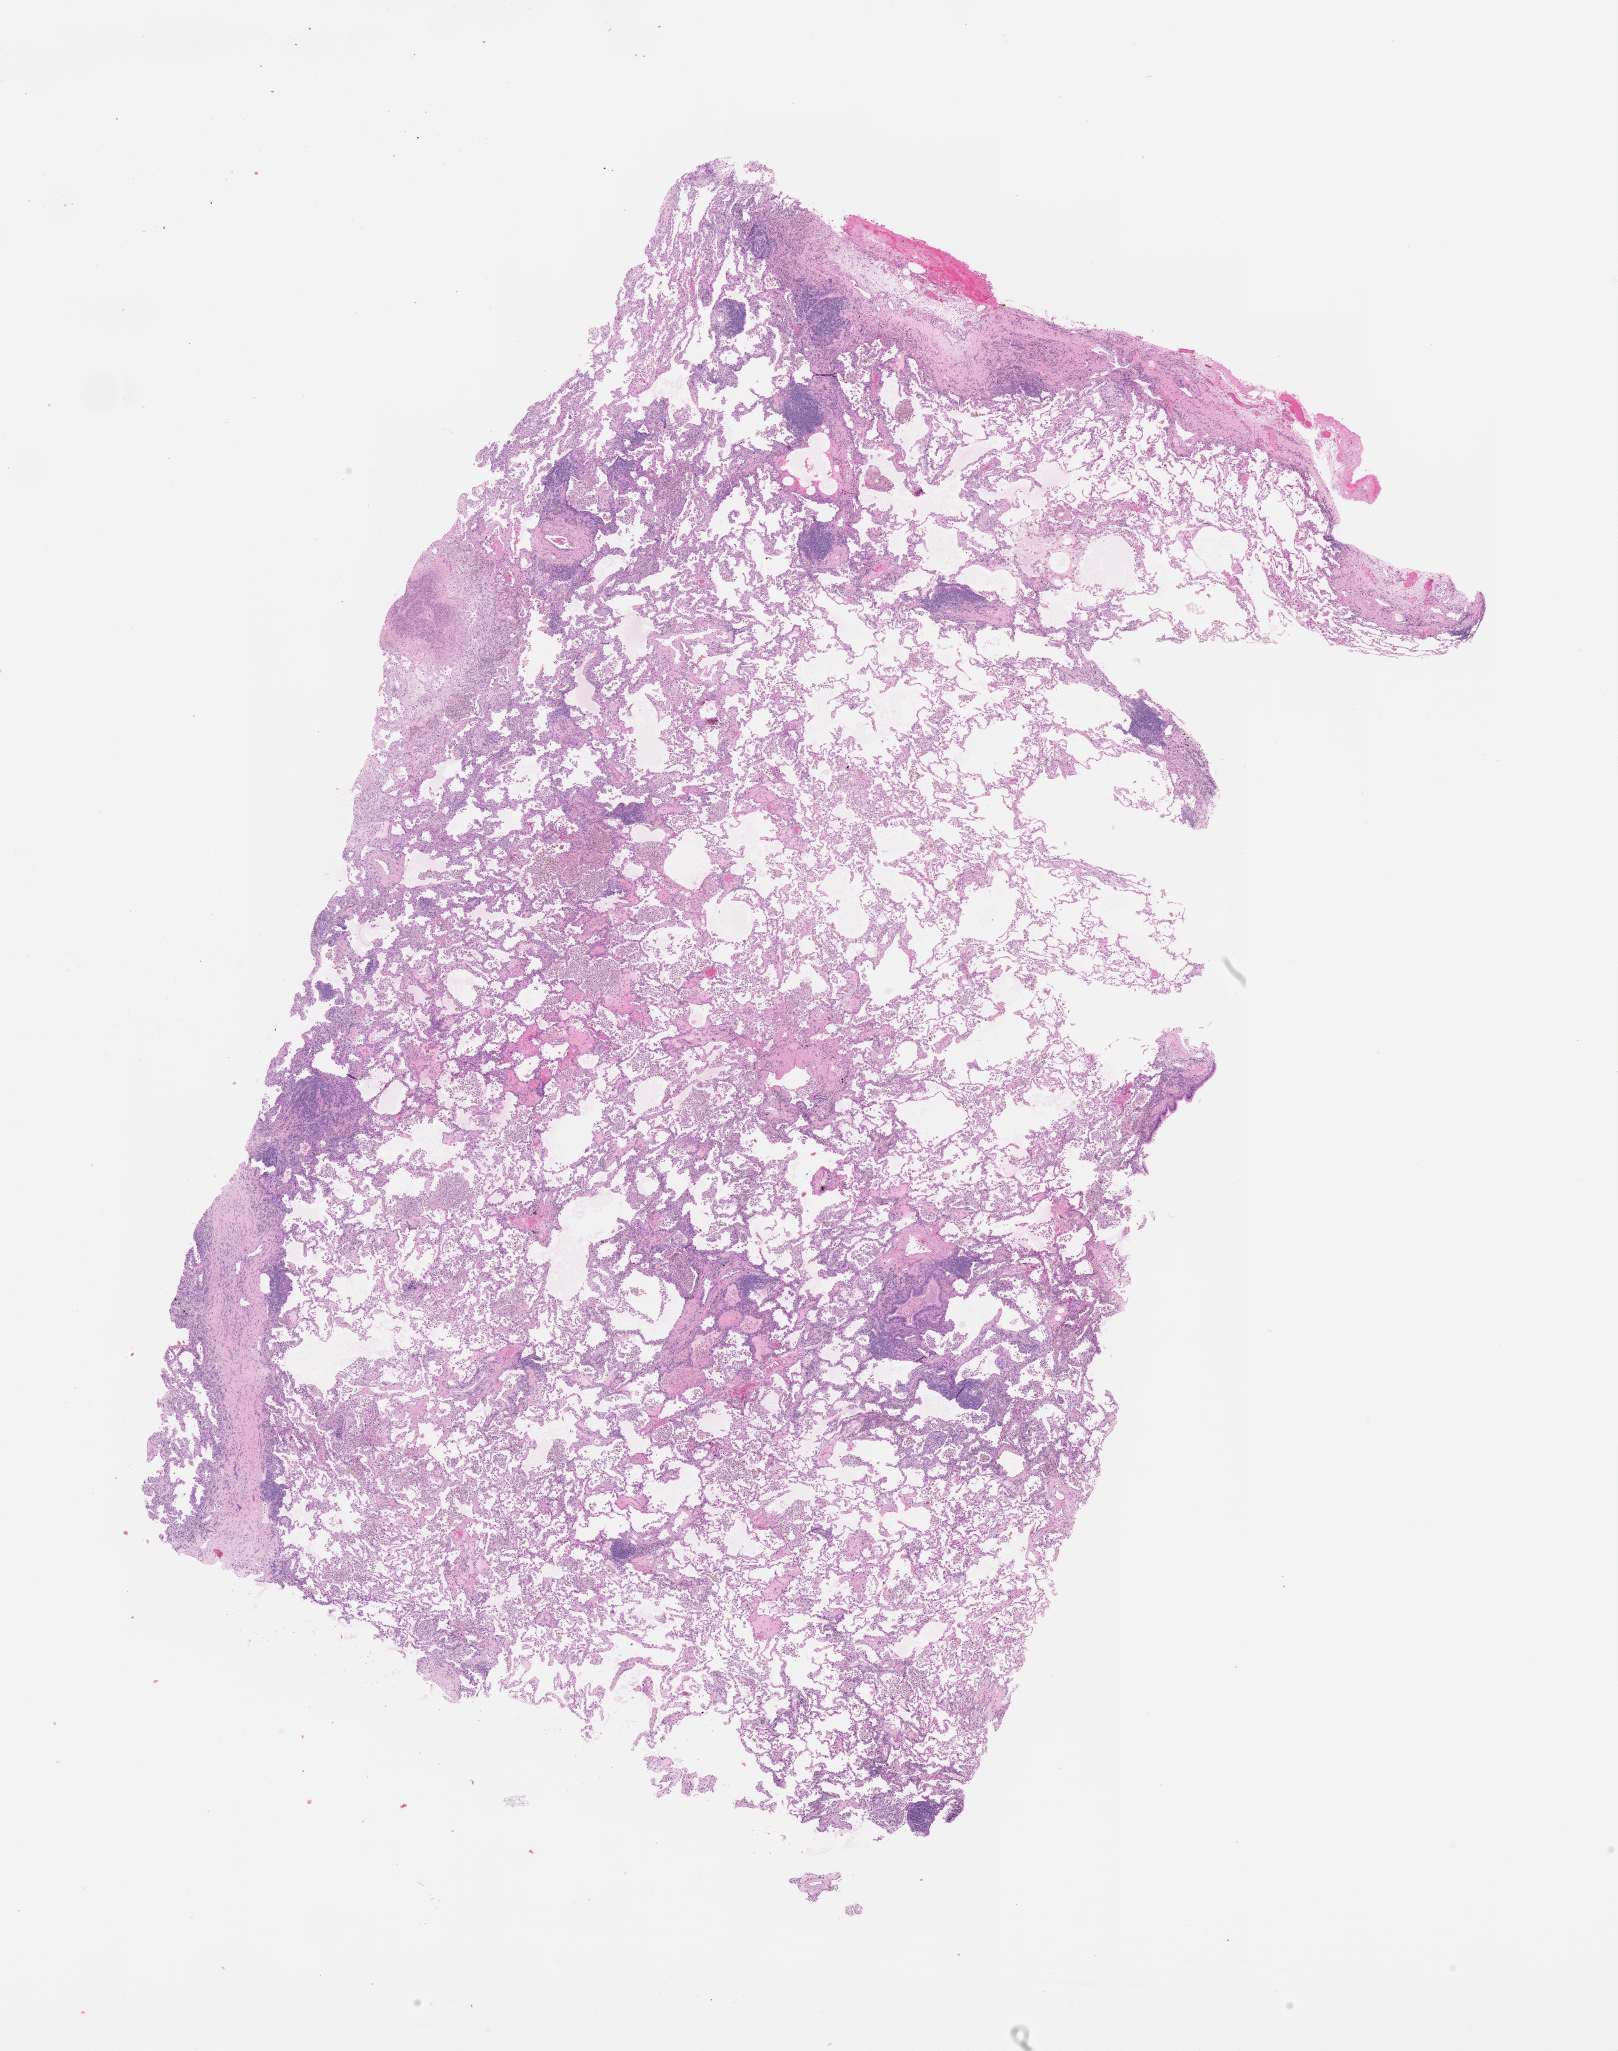
Whole-slide histology image, H&E-stained, a low-resolution overview of the entire scanned area, about 13.0 x 16.5 mm. Normal (non-tumour) tissue sample, lung. 54-year-old female patient.
This section: normal (non-tumour) tissue from the same patient. Patient diagnosis (cohort enrolment): squamous cell carcinoma (lung).